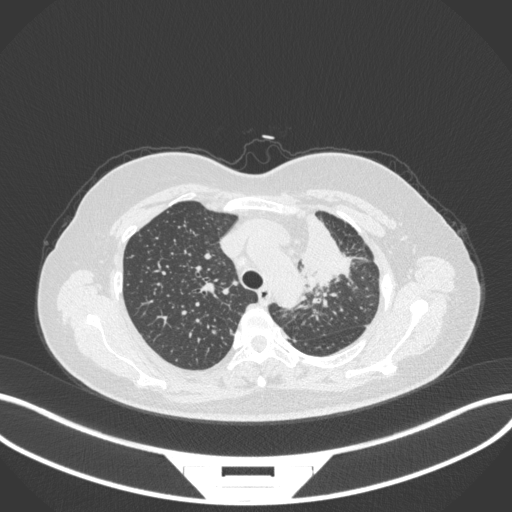
Chest CT, one axial slice; position 254 of 348 along the scan axis; reconstruction kernel B31f; lung window (W 1500 / L -600 HU); 1 mm slice thickness; 512 × 512 image matrix, field of view 400 × 400 mm. Female patient, age 49 years. From the clinical record (not read from this slice): clinical TNM (as recorded): T1c N0 M1.
Outlined on this slice (rectangle marked by the reading radiologist):
- lung tumour (recorded histology: adenocarcinoma): bounding box (x1, y1, x2, y2) in pixels: (298, 210, 358, 297)